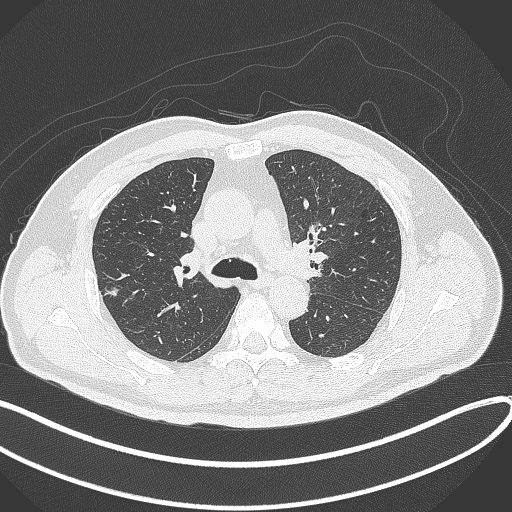
Chest CT, one axial slice. Position 225 of 372 along the scan axis. Reconstruction kernel B70f. 120 kVp. Lung window (W 1500 / L -600 HU). 1 mm slice thickness. 512 × 512 image matrix, field of view 400 × 400 mm. Patient: male, 60 years. Case-level facts recorded for this patient, not image findings: clinical TNM (as recorded): T1c N0 M0.
Annotated regions visible in this slice (bounding box drawn by a radiologist):
- lung tumour (recorded histology: adenocarcinoma): bounding box <100,282,125,303> (left, top, right, bottom; pixels)